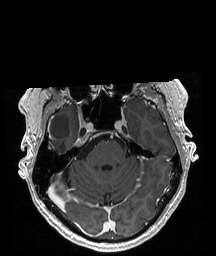
Brain MRI from a brain-tumour surgery series, one axial slice; T1-weighted post-contrast; 1 mm slice thickness; 216 × 256 image matrix, field of view 211 × 250 mm. Case-level facts recorded for this patient, not image findings: histopathology: Astrocytoma; WHO grade: 4; IDH mutation: yes; tumour location: Right Temporal.
Outlined on this slice (expert manual segmentation):
- tumour: box from (x=48, y=145) to (x=54, y=150) px